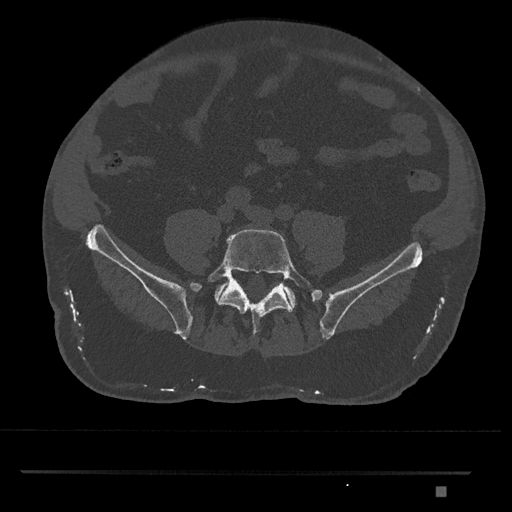
CT including the spine, one axial slice. Slice 551 of 1134 in the series (ordered by position). Reconstruction kernel Br40s/3. Bone window (W 1800 / L 400 HU). 0.5 mm slice thickness. 512 × 512 image matrix. Male patient, age 65 years. Case-level facts recorded for this patient, not image findings: primary cancer: prostate.
Structures marked on this image (semi-automatically segmented with operator editing):
- L5 vertebra: bounding box <207,229,312,337> (left, top, right, bottom; pixels)